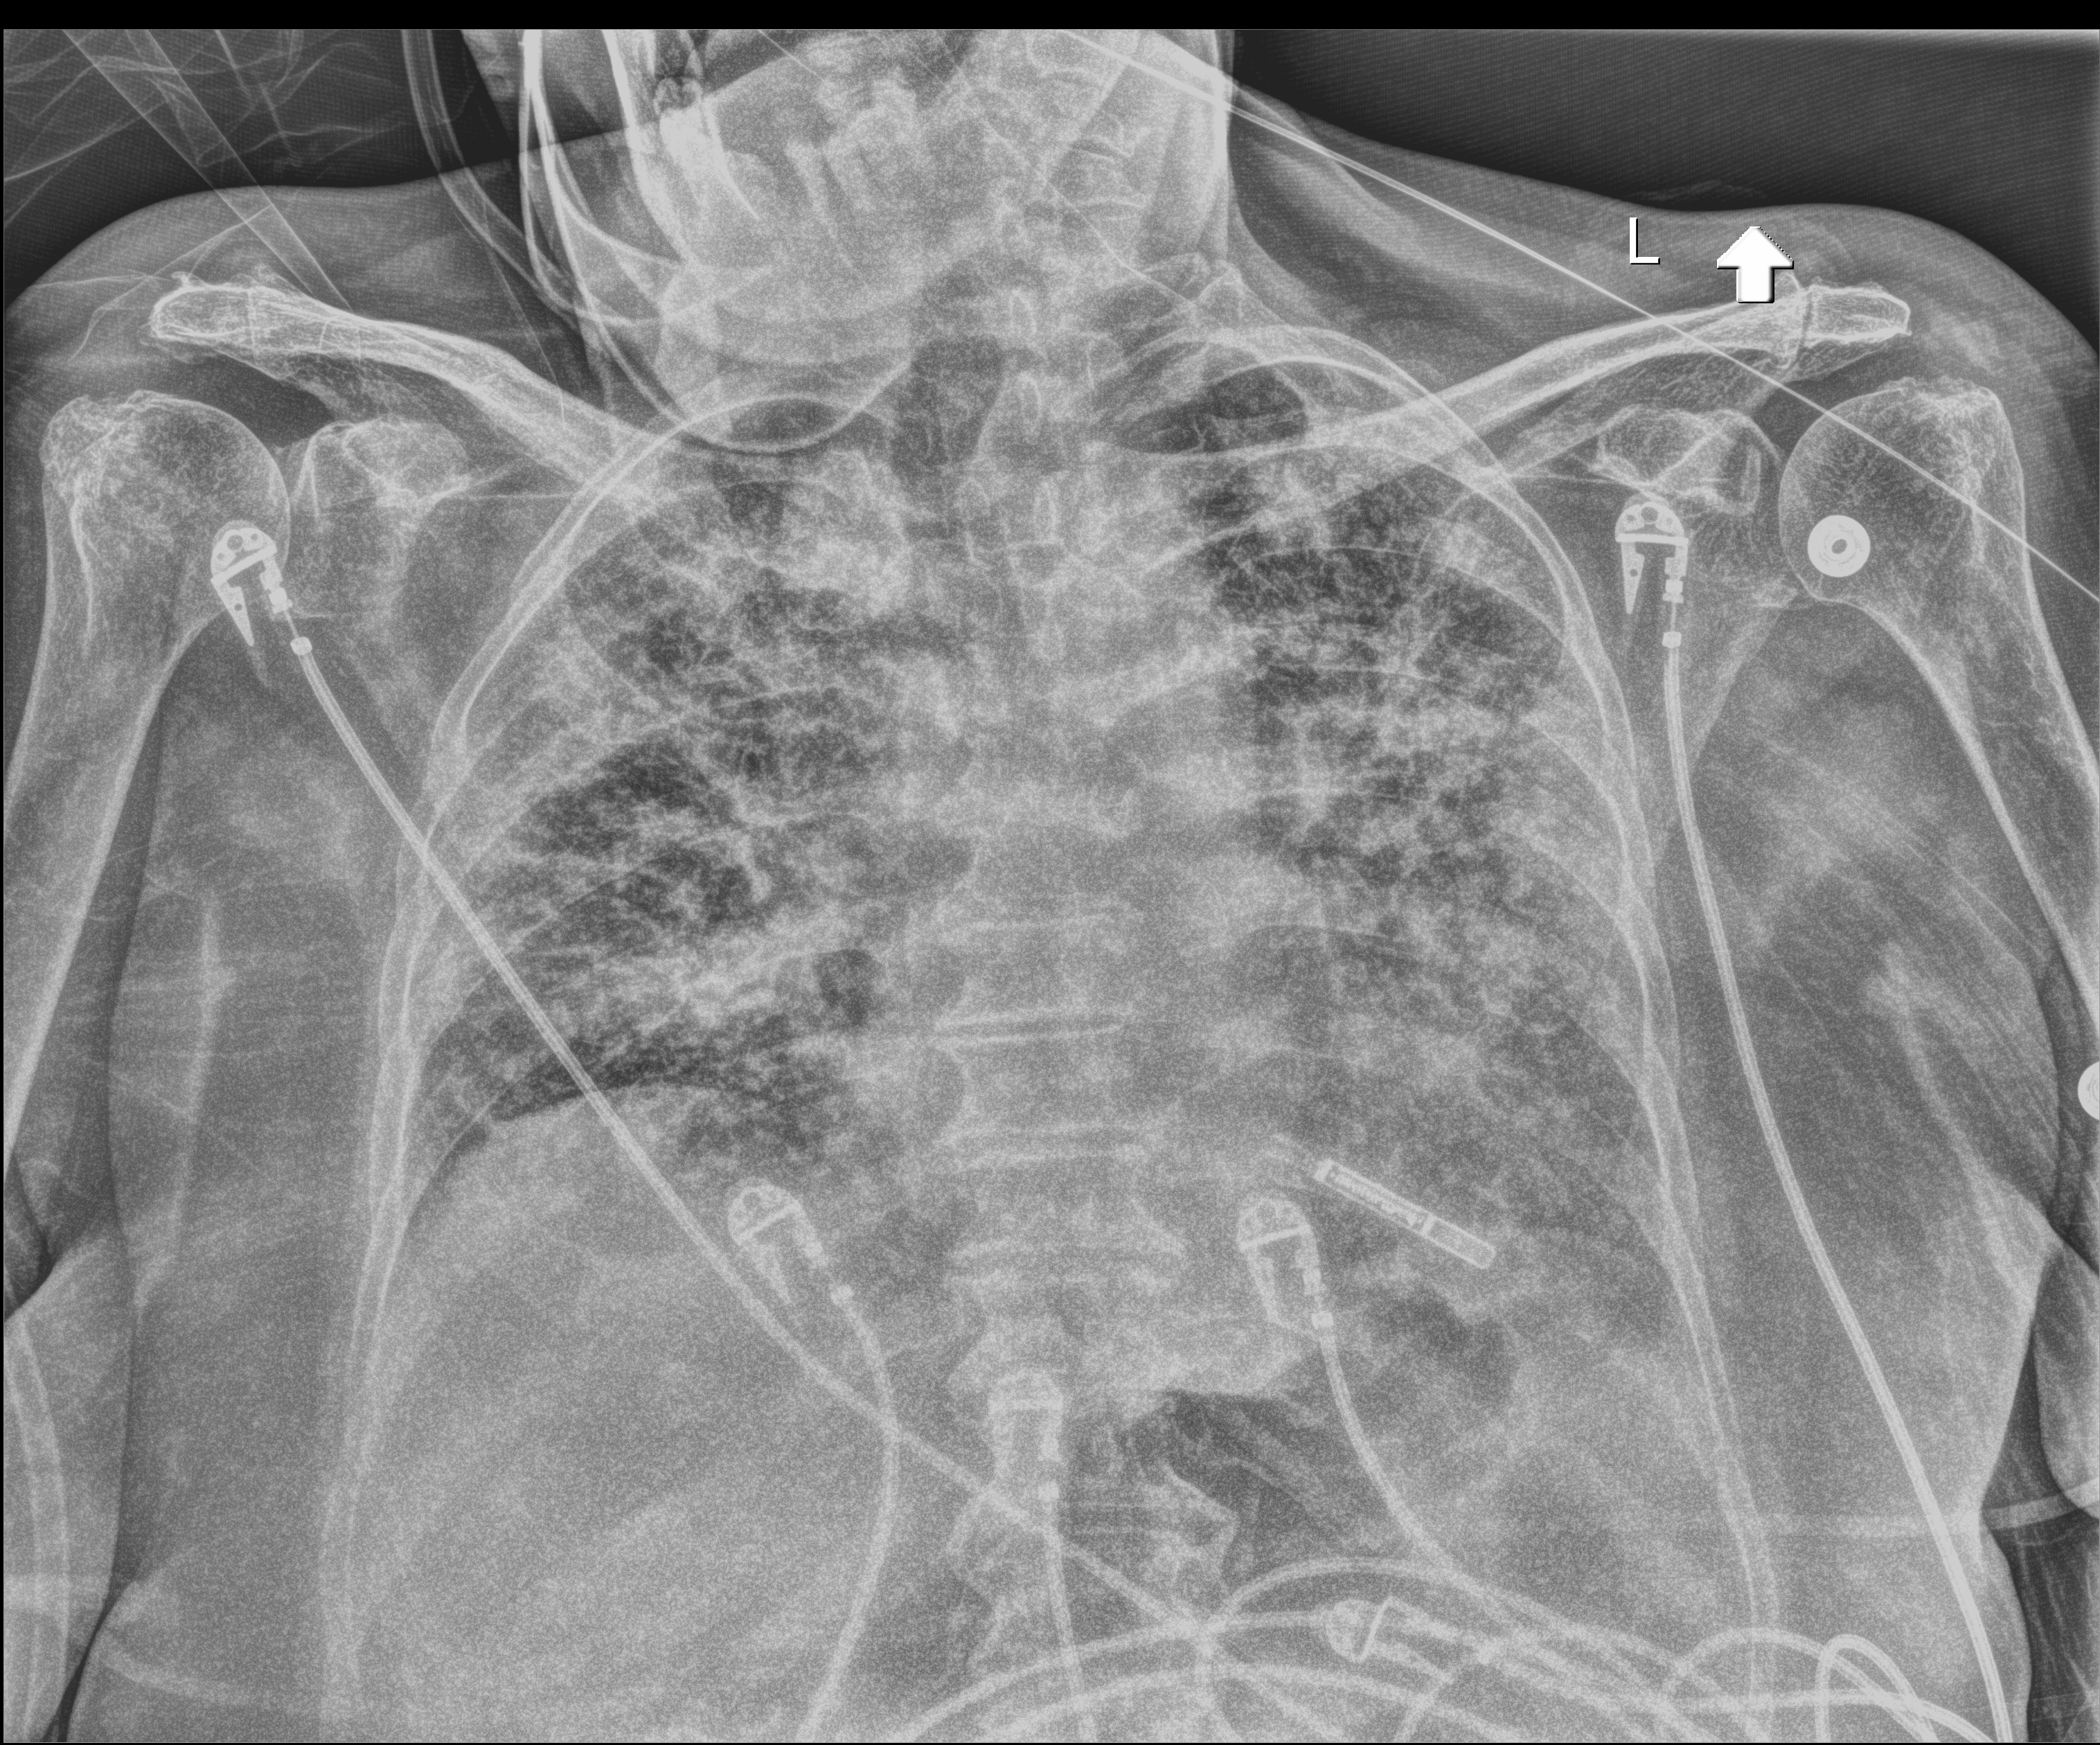
Chest radiograph; anteroposterior (AP) projection. Female patient hospitalised with COVID-19, age 75–90 years.
From the hospital-stay record, not from the radiograph (when in the stay this image was taken is not recorded):
- length of hospital stay: 10 days